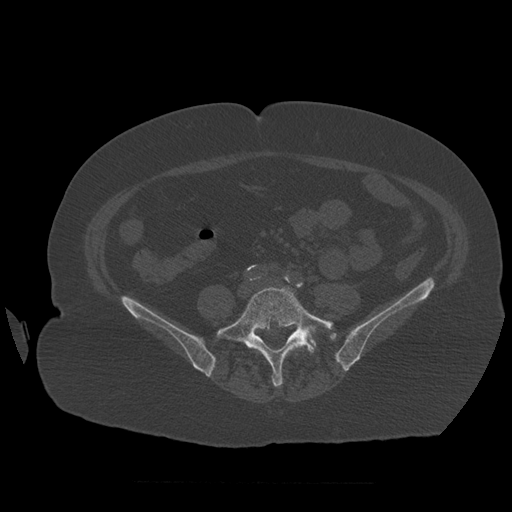
CT including the spine, one axial slice; position 184 of 399 along the scan axis; reconstruction kernel STANDARD; 120 kVp; bone window (W 1800 / L 400 HU); 1.25 mm slice thickness; 512 × 512 image matrix, field of view 404 × 404 mm. Patient age 81 years. From the clinical record (not read from this slice): primary cancer: renal; vertebrae with lytic lesions (as recorded): L1.
Annotated regions visible in this slice (semi-automatic segmentation, software-assisted and operator-edited):
- L5 vertebra: bounding box (x1, y1, x2, y2) in pixels: (217, 286, 334, 387)